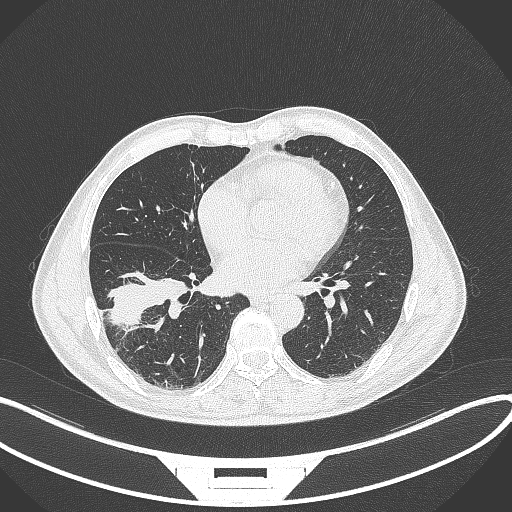
Chest CT, one axial slice; 120 kVp; lung window (W 1500 / L -600 HU); 512 × 512 image matrix, field of view 400 × 400 mm. Patient: male, 58 years. From the clinical record (not read from this slice): clinical TNM (as recorded): T3 N0 M0; histopathological grade: G2.
Structures marked on this image (rectangle marked by the reading radiologist):
- lung tumour (recorded histology: squamous cell carcinoma): bounding box <108,271,194,331> (left, top, right, bottom; pixels)